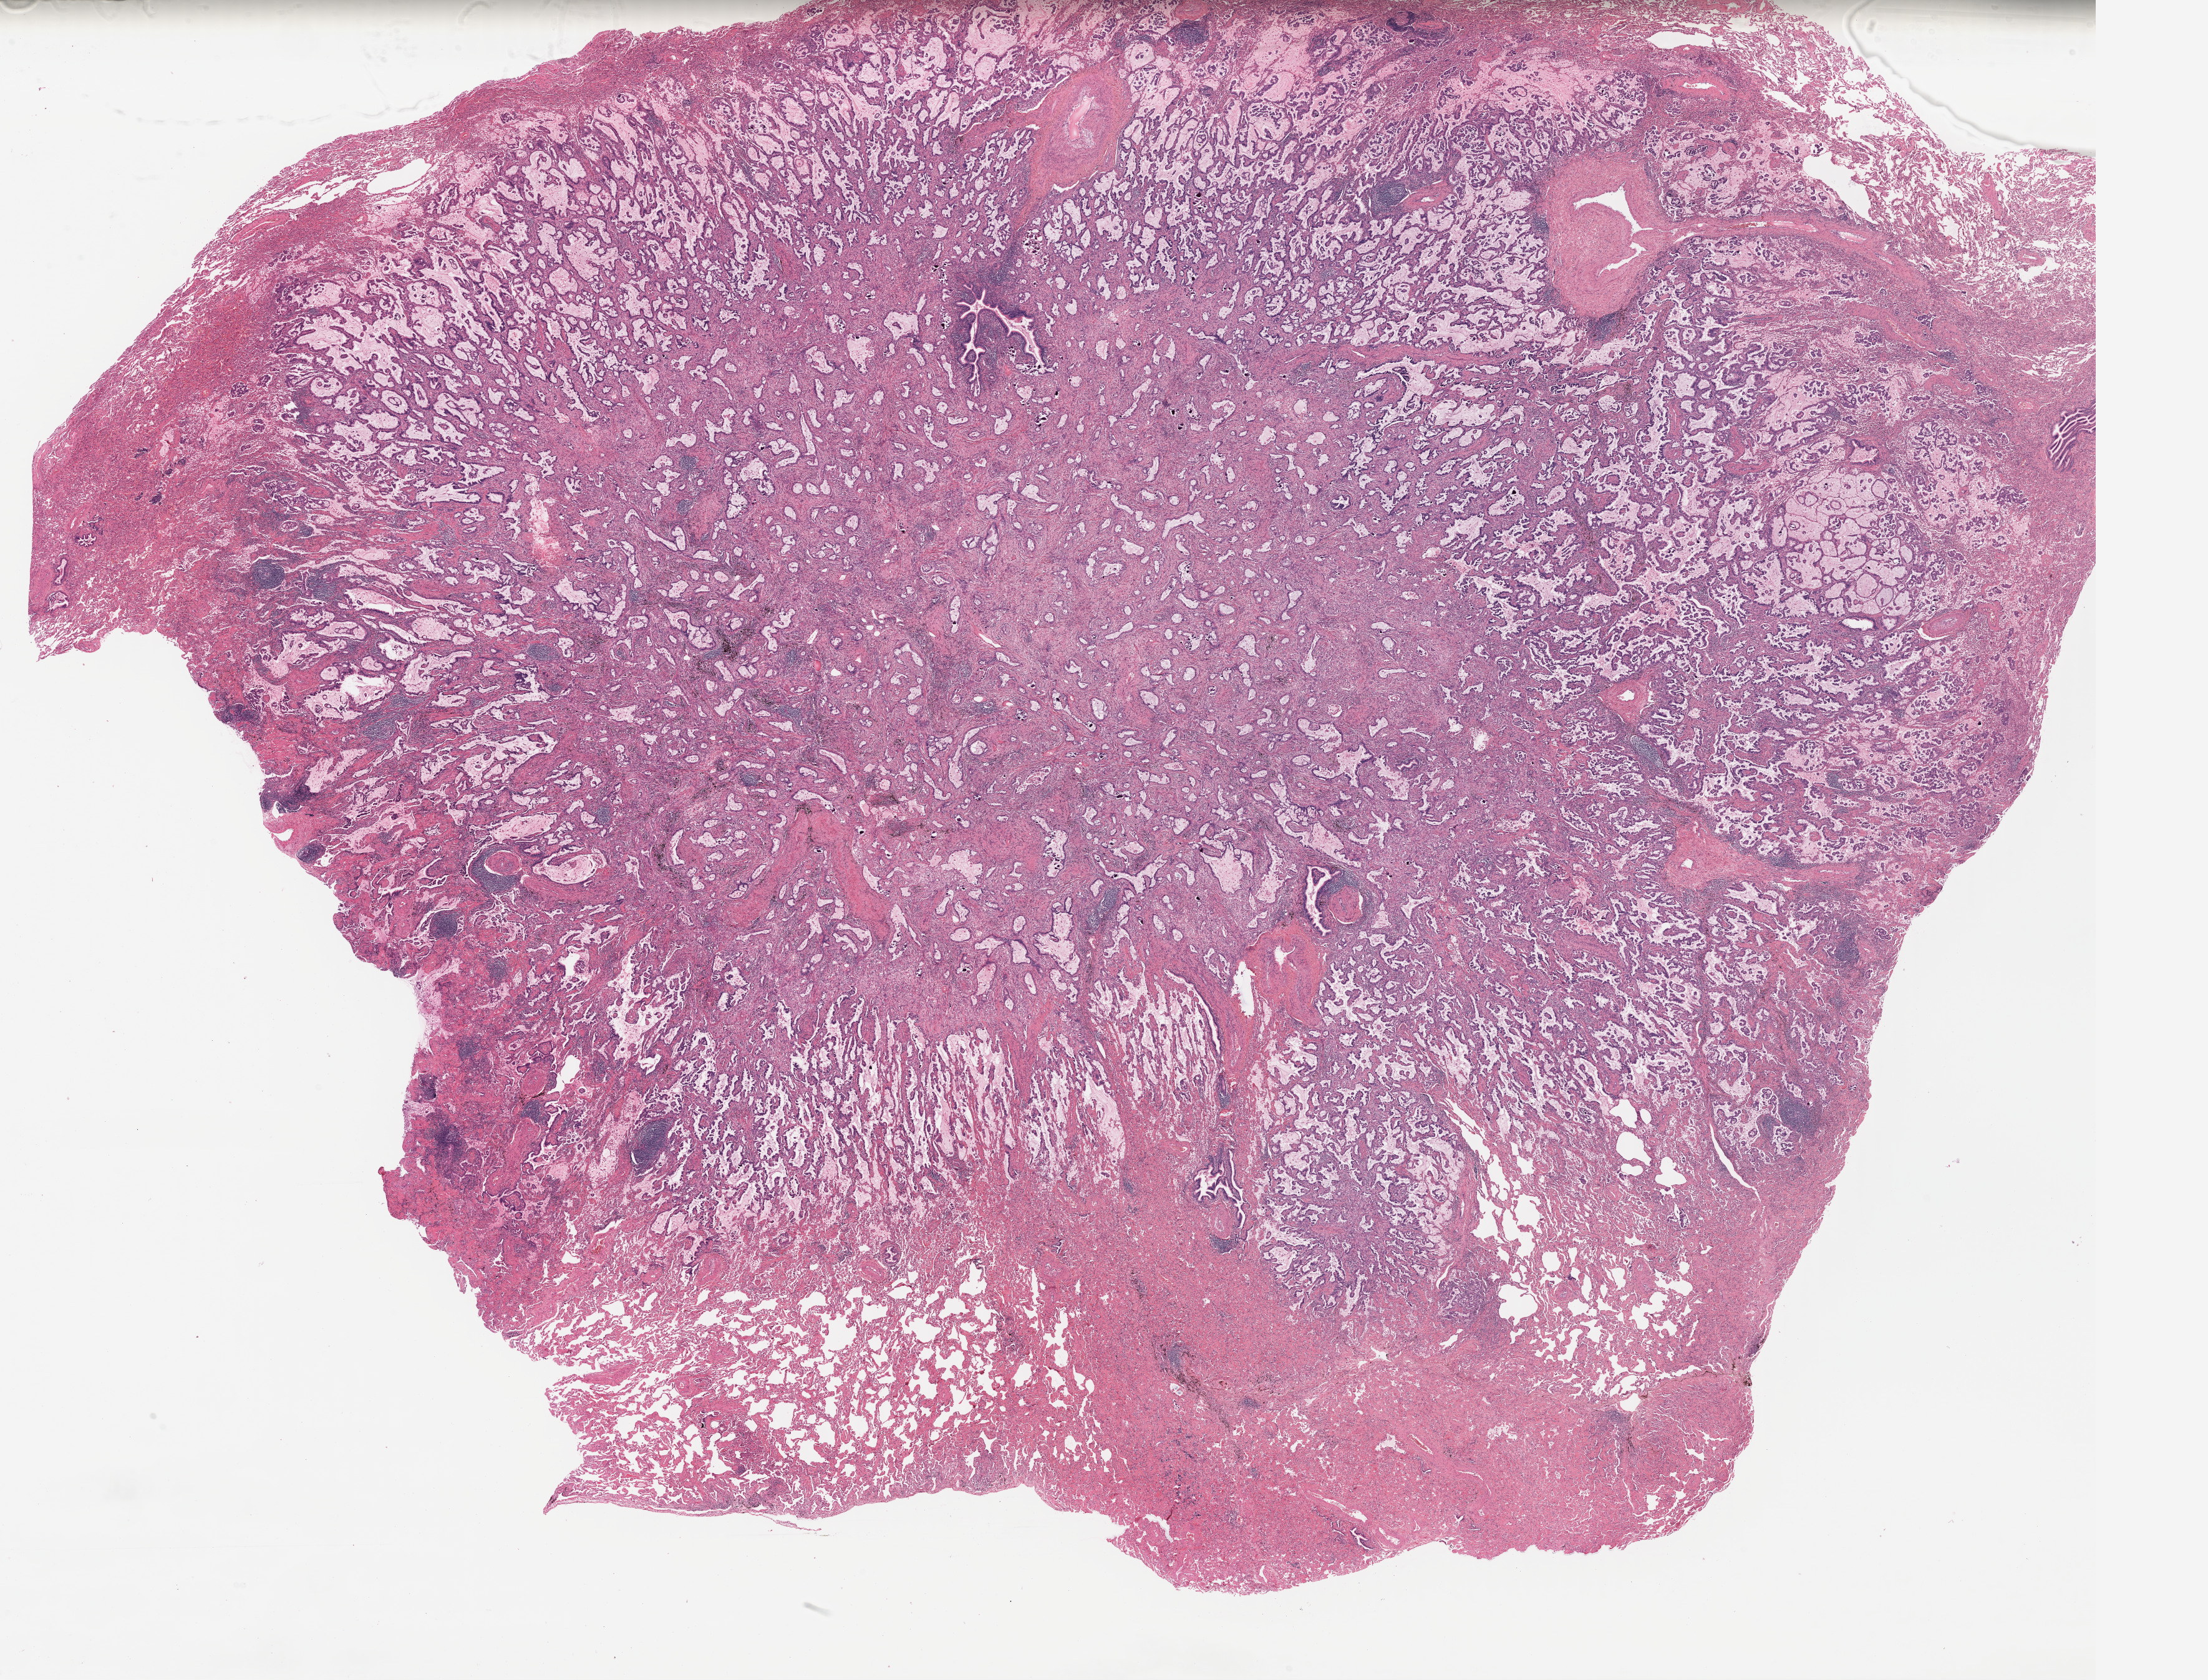
Digitized Hematoxylin and eosin (H&E) stained tissue section (whole slide), a low-resolution overview of the entire scanned area, about 27.8 x 21.2 mm. FFPE section. Lung, primary tumour sample. Female, age 77 years at initial diagnosis.
Histologic diagnosis: Adenocarcinoma with mixed subtypes (lower lobe, lung). TNM: T1 N0 M0. AJCC pathologic stage: IA (6th edition).